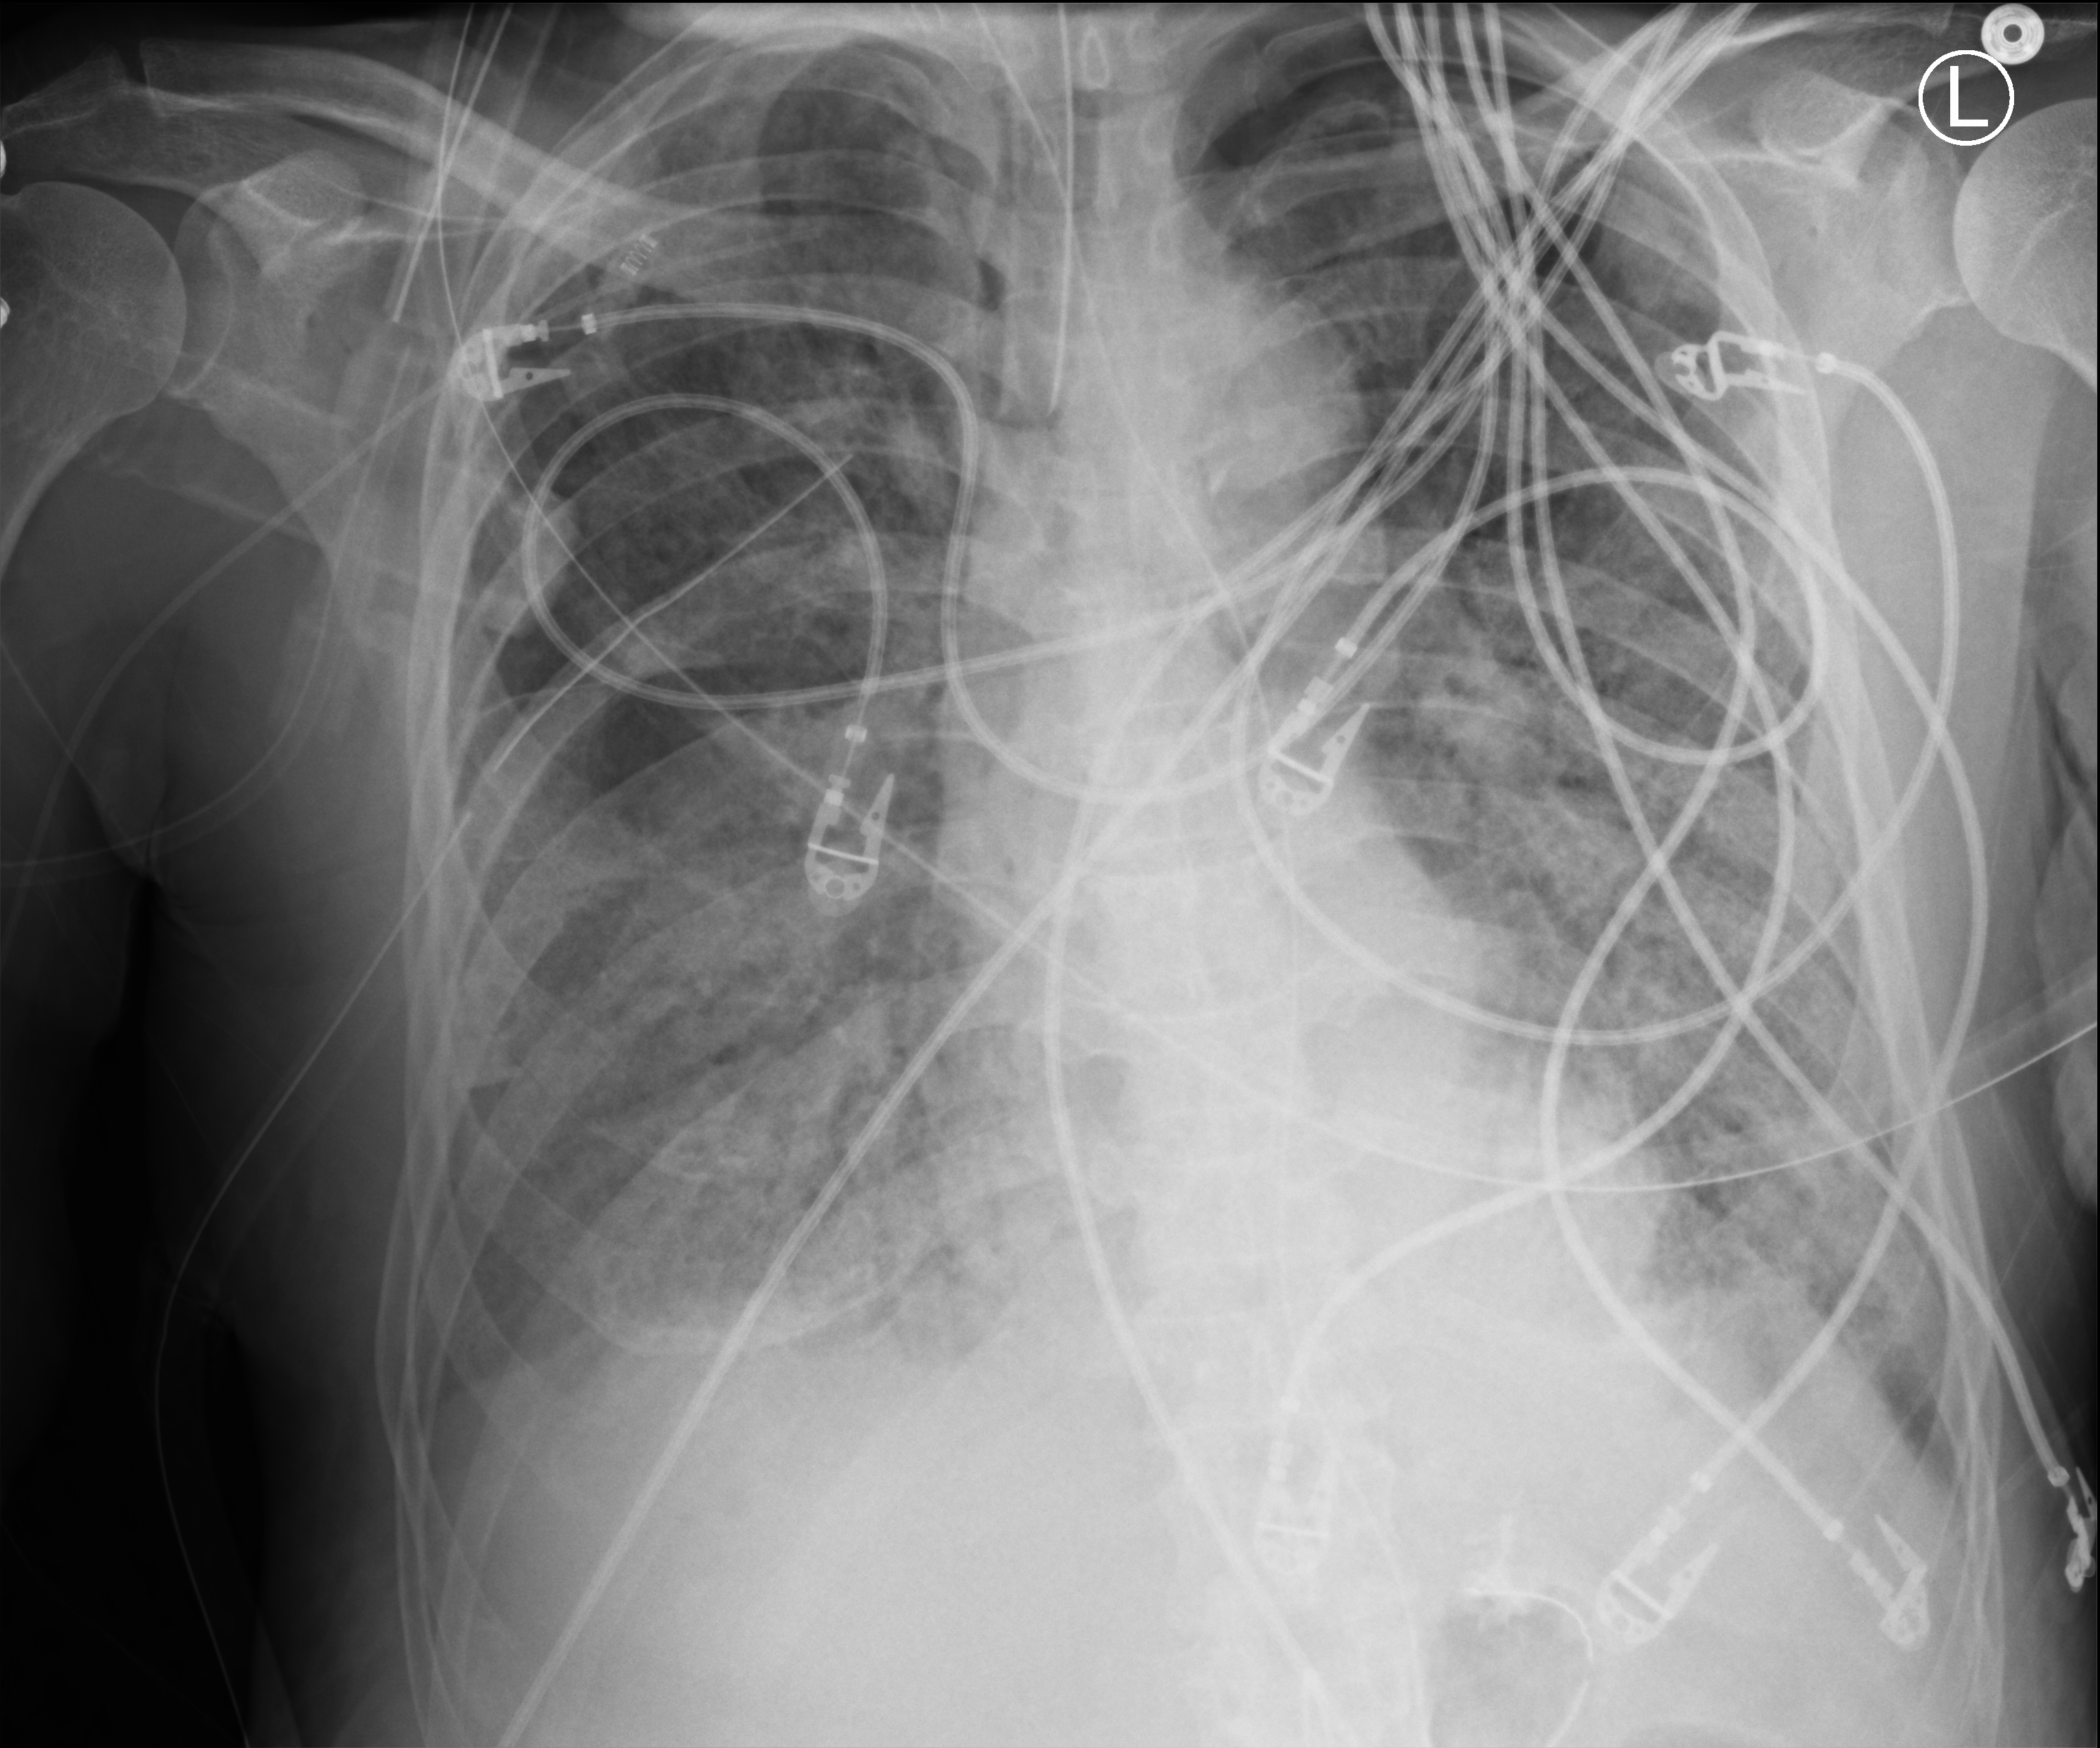
Bedside chest radiograph (computed radiography); anteroposterior (AP) projection. Male patient hospitalised with COVID-19, age 60–74 years.
From the hospital-stay record, not from the radiograph (when in the stay this image was taken is not recorded): mechanically ventilated during this hospital stay: yes; admitted to intensive care during this hospital stay: yes; length of hospital stay: 31 days.